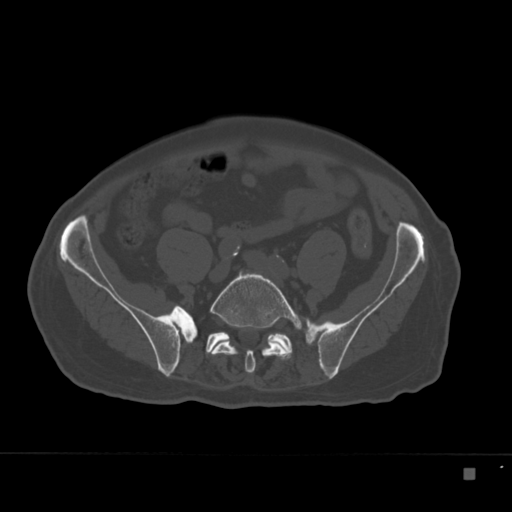
CT including the spine, one axial slice; 120 kVp; bone window (W 1800 / L 400 HU); 1.5 mm slice thickness; 512 × 512 image matrix. Patient: male, 72 years. Case-level facts recorded for this patient, not image findings: primary cancer: skeletal.
Structures marked on this image (semi-automatic segmentation, software-assisted and operator-edited):
- L5 vertebra: bounding box <209,271,302,373> (left, top, right, bottom; pixels)